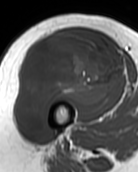
MRI of an extremity soft-tissue mass, one axial slice; position 58 of 99 along the scan axis; MR volume resampled by the dataset authors to the PET/CT grid (not the native acquisition matrix); 3.27 mm slice thickness; 138 × 172 image matrix, field of view 135 × 168 mm. Female patient. From the clinical record (not read from this slice): histological type: pleiomorphic undifferentiated sarcoma; grade: high; site of the primary tumour: right quadricep.
Structures marked on this image (expert contour drawn on MRI and transferred to this co-registered scan by the dataset authors):
- gross tumour volume including surrounding oedema: bounding box <16,32,122,133> (left, top, right, bottom; pixels)
- gross tumour volume (mass): <16,32,122,133>